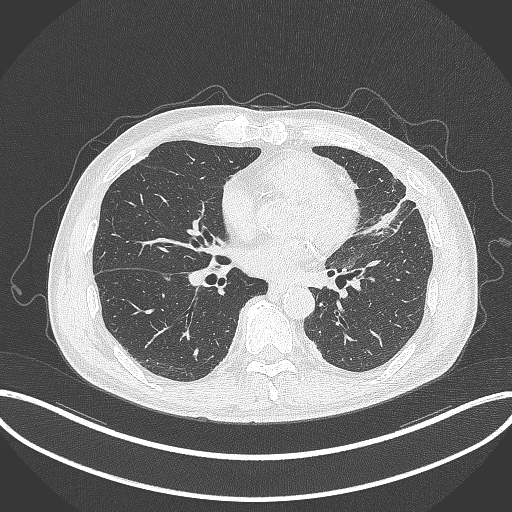
Chest CT, one axial slice; slice 145 of 382 in the series (ordered by position); reconstruction kernel B70f; lung window (W 1500 / L -600 HU); 1 mm slice thickness; 512 × 512 image matrix, field of view 415 × 415 mm. Patient: male, 64 years. From the clinical record (not read from this slice): clinical TNM (as recorded): T4 N1 M0; histopathological grade: G3.
Outlined on this slice (bounding box drawn by a radiologist):
- lung tumour (recorded histology: adenocarcinoma): bounding box [x1, y1, x2, y2] px = [358, 191, 417, 241]